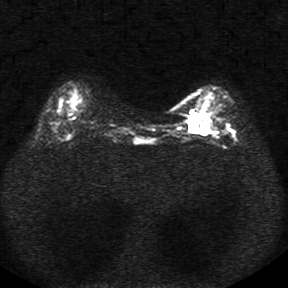
Breast MRI, one axial slice; diffusion-weighted series; image 2 of 4 stored at this slice position (different b-values; order by instance number); 1.5 T; 5 mm slice thickness; 288 × 288 image matrix. Female patient.
Outlined on this slice (manually delineated by an expert):
- tumour on diffusion-weighted imaging: bounding box [x1, y1, x2, y2] px = [189, 119, 196, 131]